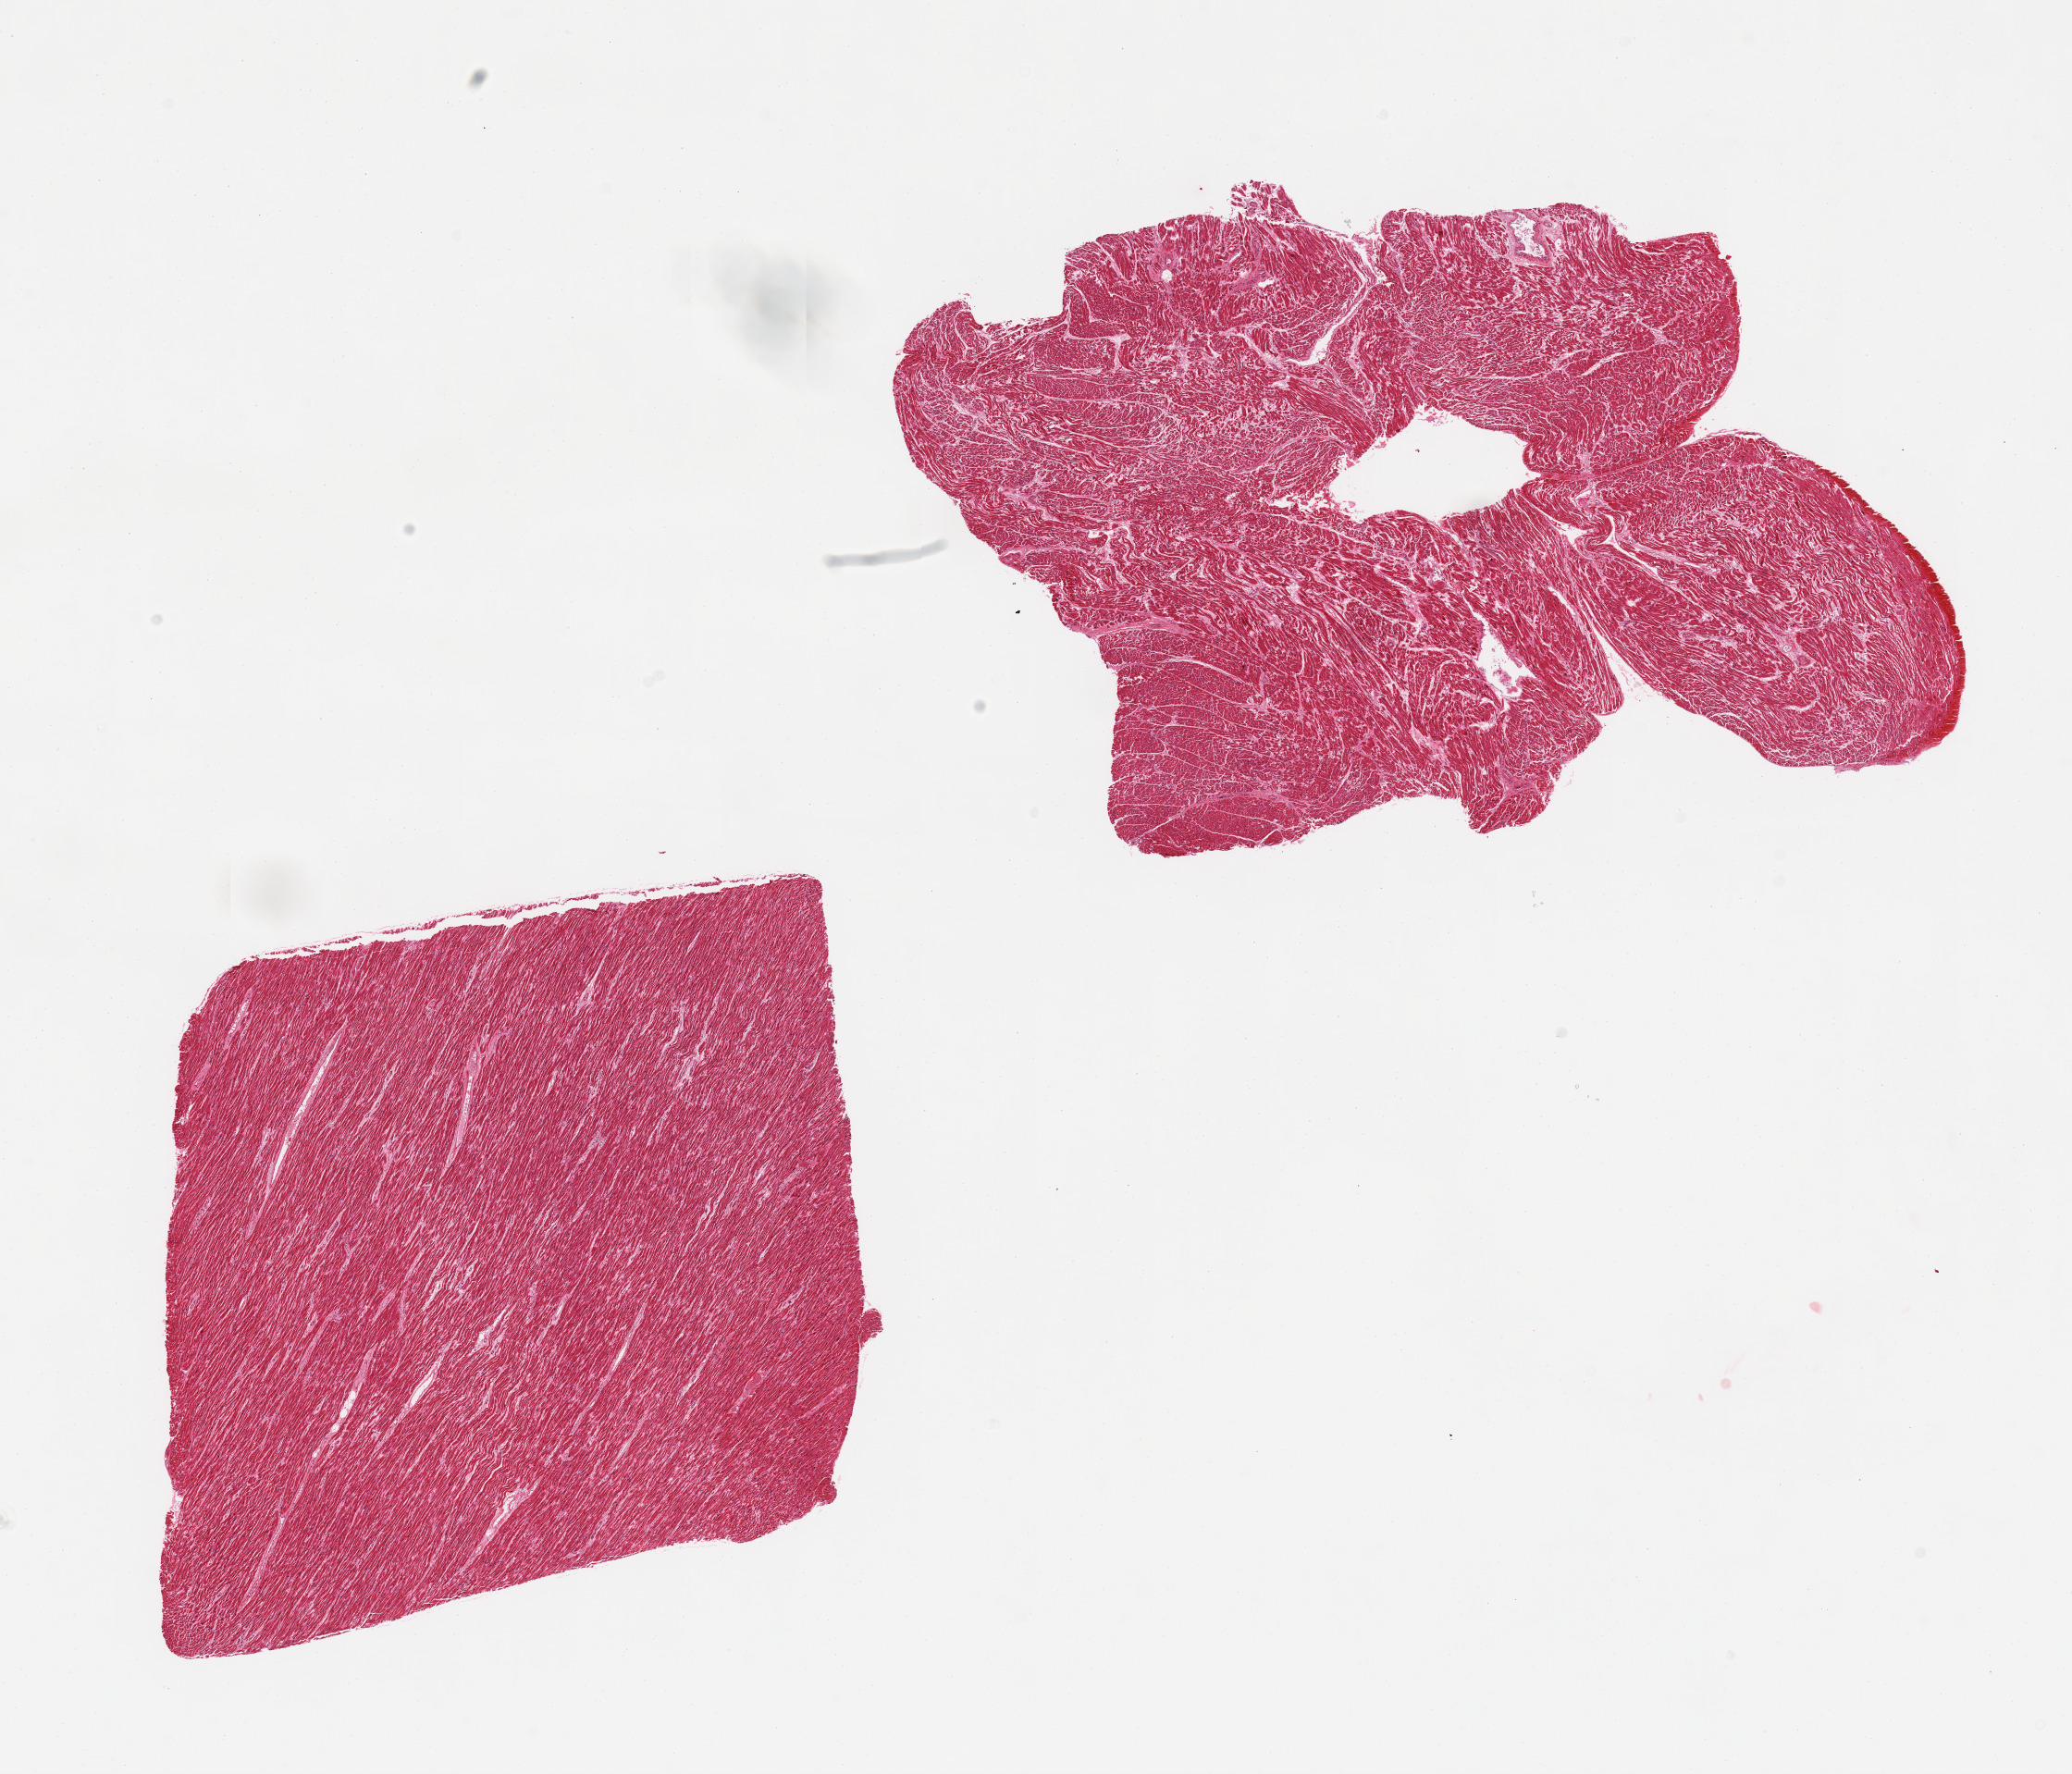
Digitized hematoxylin and eosin (H&E)-stained section, brightfield — low-resolution overview of the scanned area, about 17.7 x 15.2 mm (slide scanned at 20x), PAXgene-fixed paraffin-embedded (PFPE) section, section of heart (target tissue), donor tissue sample. Donor sex: female.
Review note (as recorded): 2 pieces.